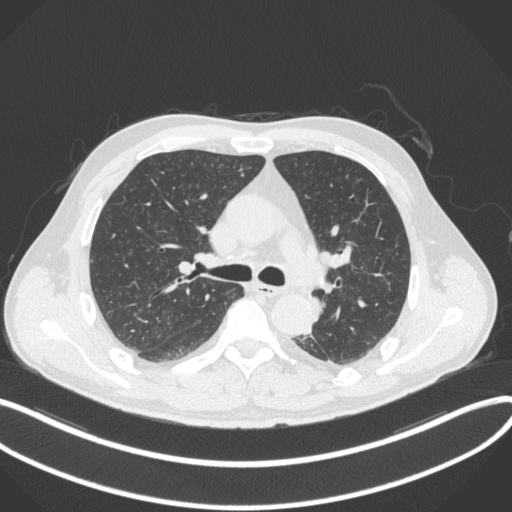
Chest CT, one axial slice. Position 224 of 328 along the scan axis. Lung window (W 1500 / L -600 HU). 1 mm slice thickness. 512 × 512 image matrix. Patient: male, 59 years. From the clinical record (not read from this slice): clinical TNM (as recorded): T2a N2 M0.
Outlined on this slice (rectangle marked by the reading radiologist):
- lung tumour (recorded histology: squamous cell carcinoma): bounding box <309,295,326,326> (left, top, right, bottom; pixels)